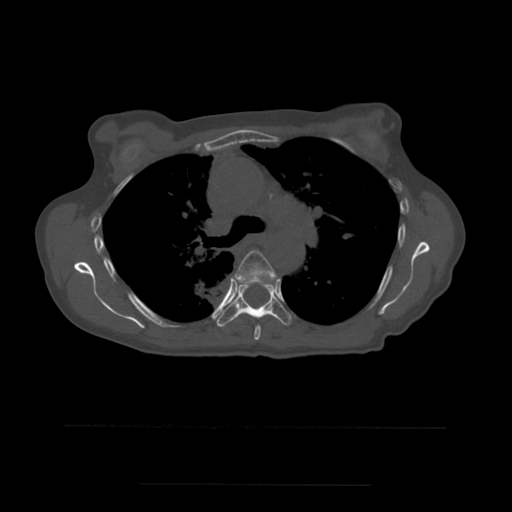
CT including the spine, one axial slice; slice 382 of 544 in the series (ordered by position); bone window (W 1800 / L 400 HU); 1.25 mm slice thickness; 512 × 512 image matrix, field of view 350 × 350 mm. Patient age 58 years. From the clinical record (not read from this slice): primary cancer: lung.
Outlined on this slice (semi-automatic segmentation, software-assisted and operator-edited):
- T5 vertebra: bounding box (x1, y1, x2, y2) in pixels: (233, 250, 277, 341)
- T6 vertebra: (217, 278, 291, 327)